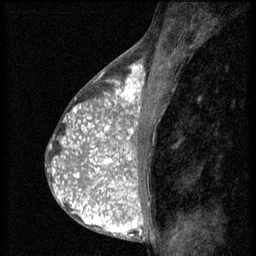
Breast MRI (dynamic contrast-enhanced), one sagittal slice; slice 31 of 60 in the series (ordered by position); 3 images stored at this slice position (order not interpretable as contrast timing); 1.5 T; TE 4.2 ms, TR 8.2 ms; 2 mm slice thickness; 256 × 256 image matrix. Female patient, age 38 years.
Outlined on this slice (semi-automatic segmentation, software-assisted and operator-edited):
- analysis volume of interest (the breast-tissue region the enhancement analysis was run in; not a lesion): bounding box [x1, y1, x2, y2] px = [92, 112, 152, 171]
- tumour enhancement mask (voxels above the 70 % enhancement threshold inside the analysis volume of interest): [92, 112, 140, 171]